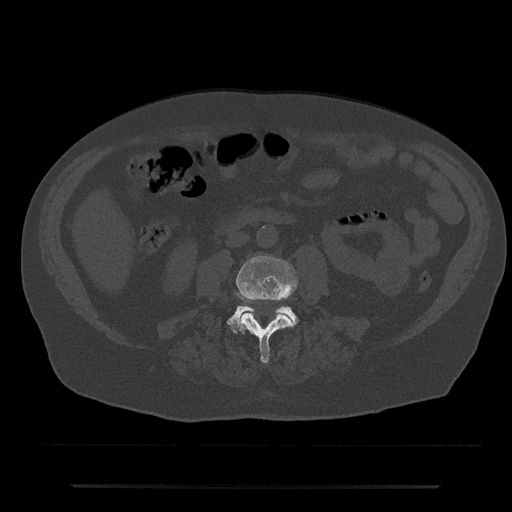
CT including the spine, one axial slice. Position 387 of 797 along the scan axis. Reconstruction kernel Br40s/3. 120 kVp. Bone window (W 1800 / L 400 HU). 0.5 mm slice thickness. 512 × 512 image matrix, field of view 434 × 434 mm. Male patient, age 80 years. Case-level facts recorded for this patient, not image findings: primary cancer: prostate; vertebrae with lytic lesions (as recorded): L1, T11.
Structures marked on this image (semi-automatically segmented with operator editing):
- L3 vertebra: box from (x=236, y=256) to (x=298, y=363) px
- L4 vertebra: (x=227, y=305)–(x=299, y=332)